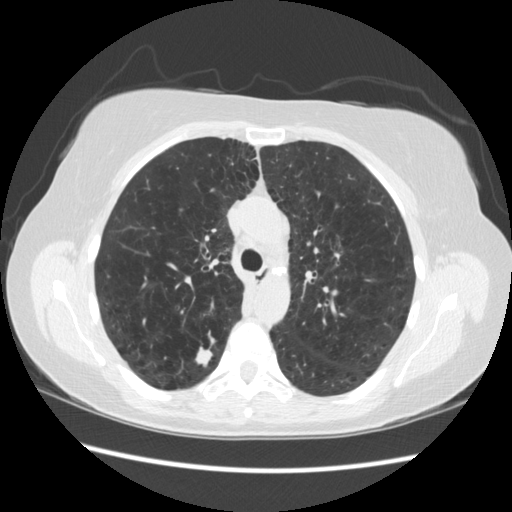
Low-dose screening chest CT, one axial slice. Position 162 of 235 along the scan axis. Reconstruction kernel STANDARD. Lung window (W 1500 / L -600 HU). 512 × 512 image matrix, field of view 360 × 360 mm.
Annotated regions visible in this slice (manually delineated by an expert):
- lesion 1 (tumor, upper lobe of right lung): box from (x=196, y=346) to (x=213, y=365) px